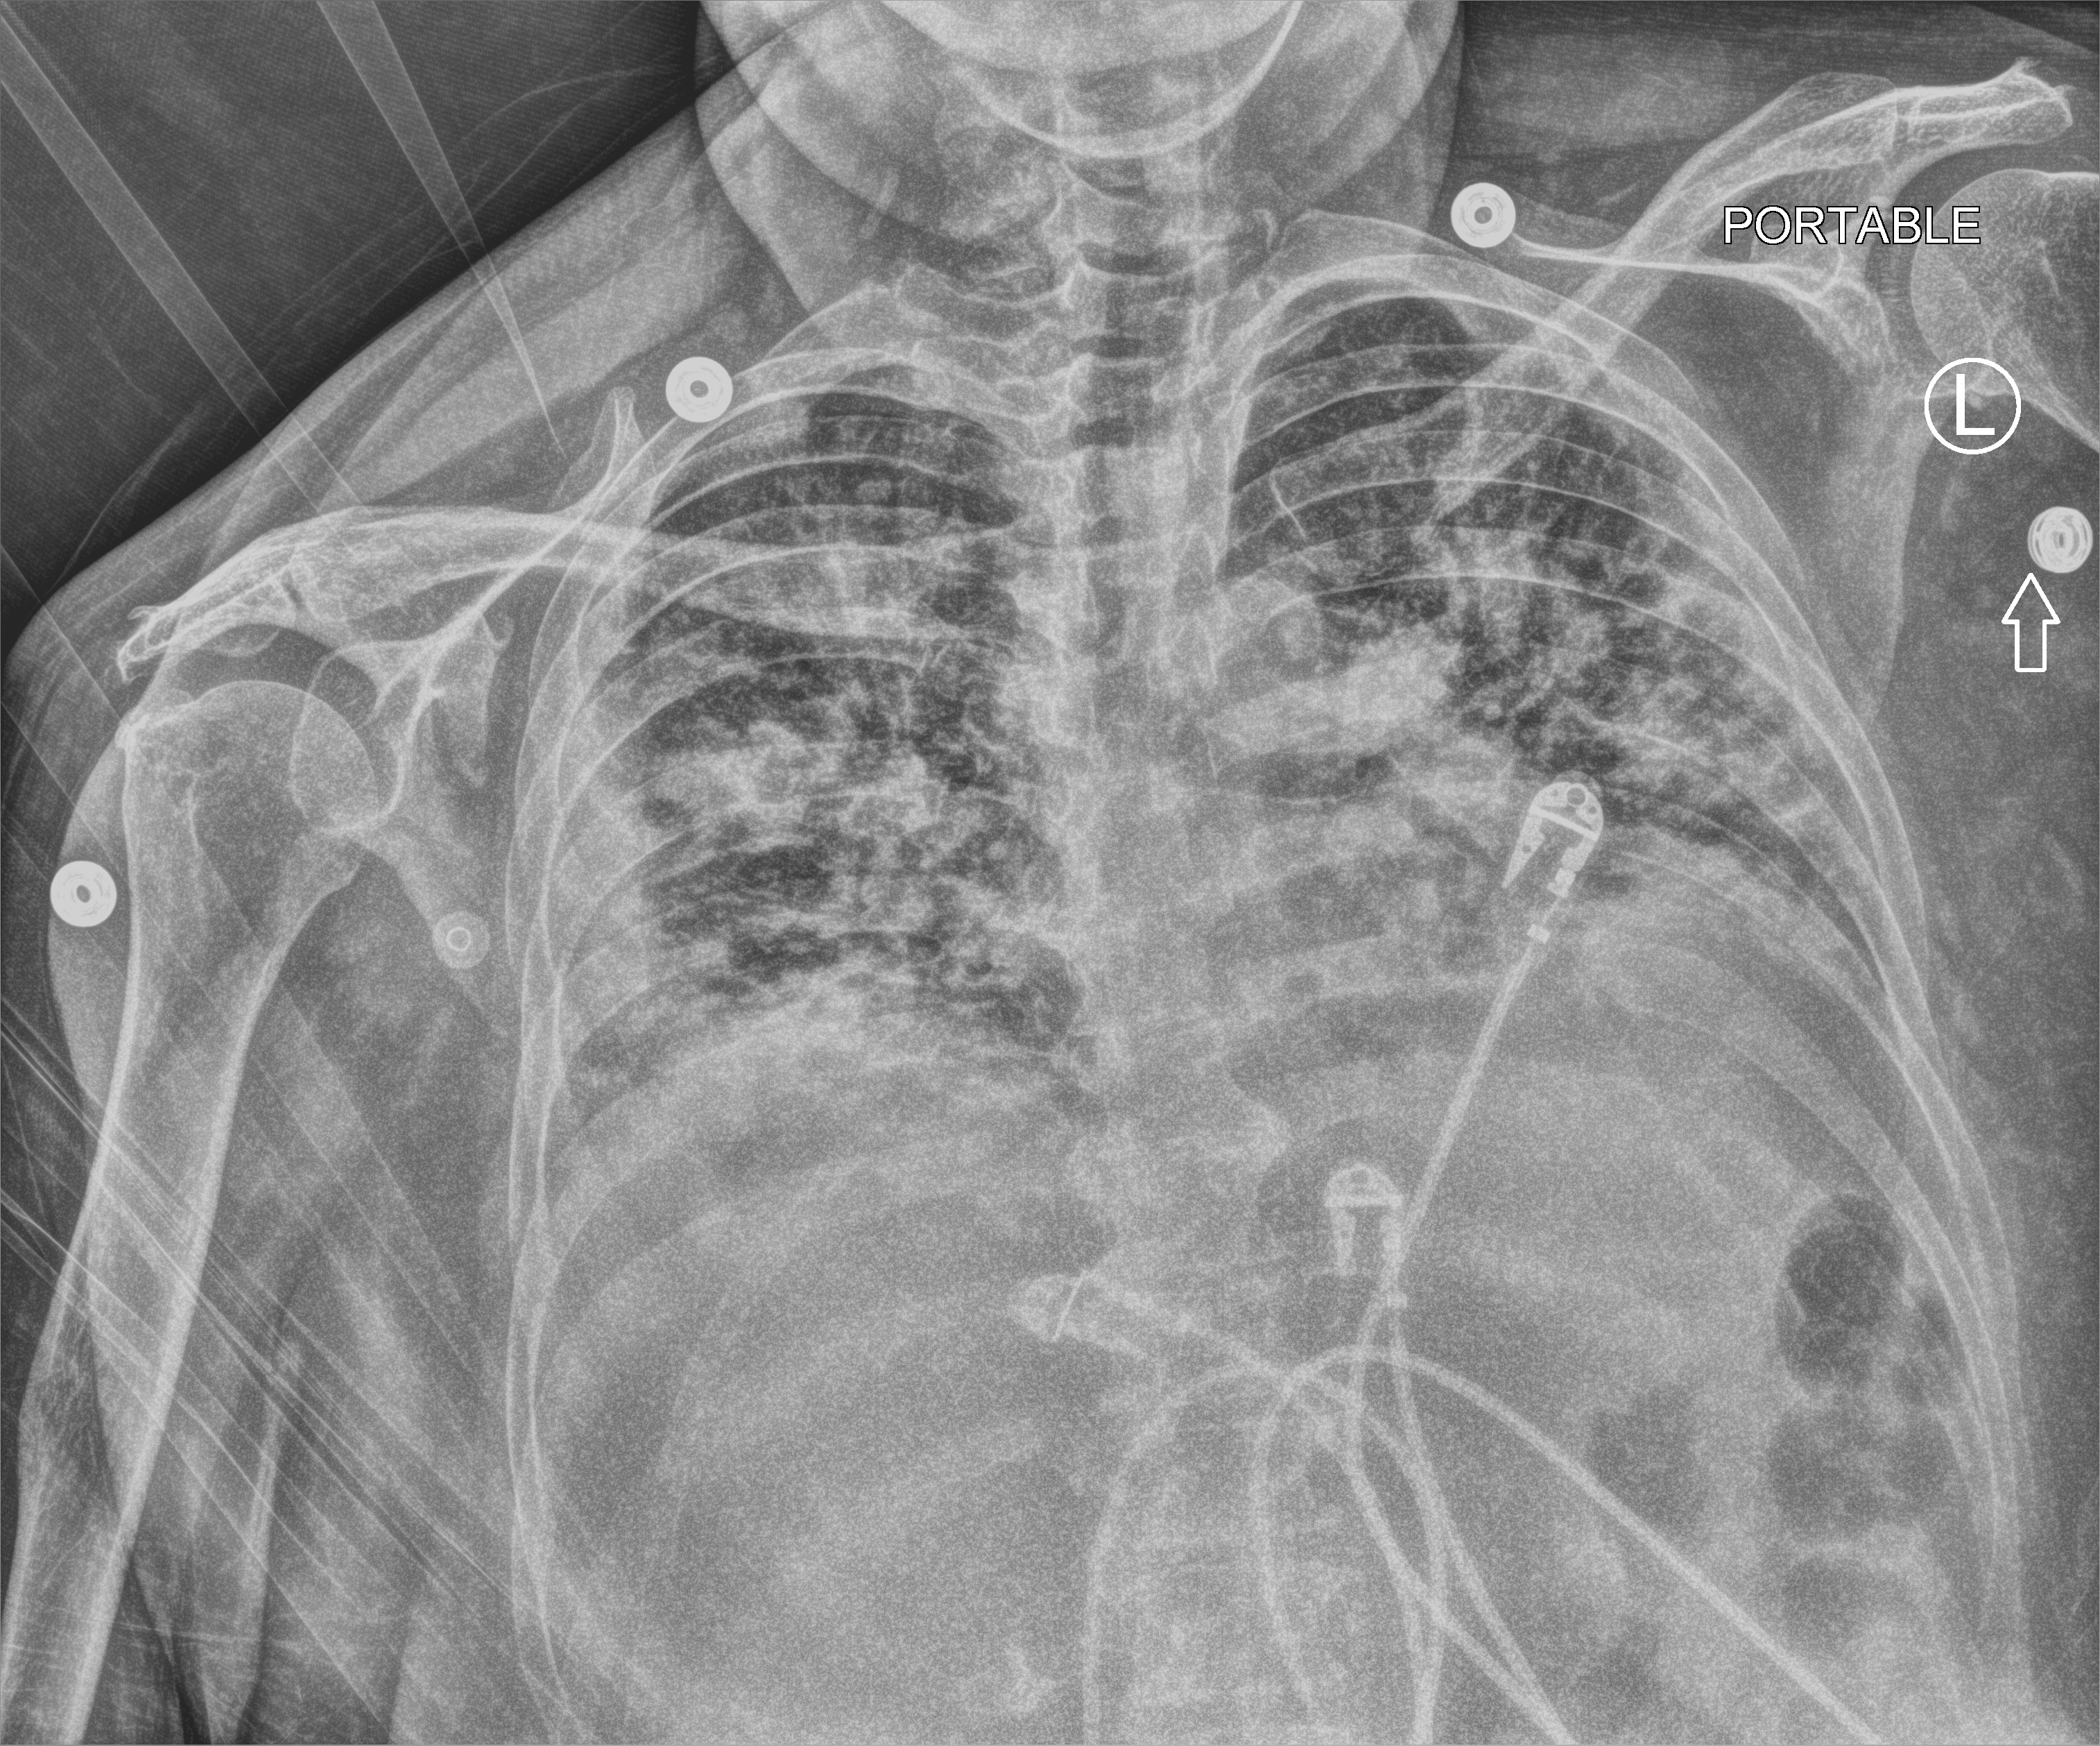
Chest X-ray (portable); anteroposterior (AP) projection. Patient hospitalised with COVID-19; female, aged 18–59 years.
From the hospital-stay record, not from the radiograph (when in the stay this image was taken is not recorded):
- length of hospital stay: 12 days
- mechanically ventilated during this hospital stay: no